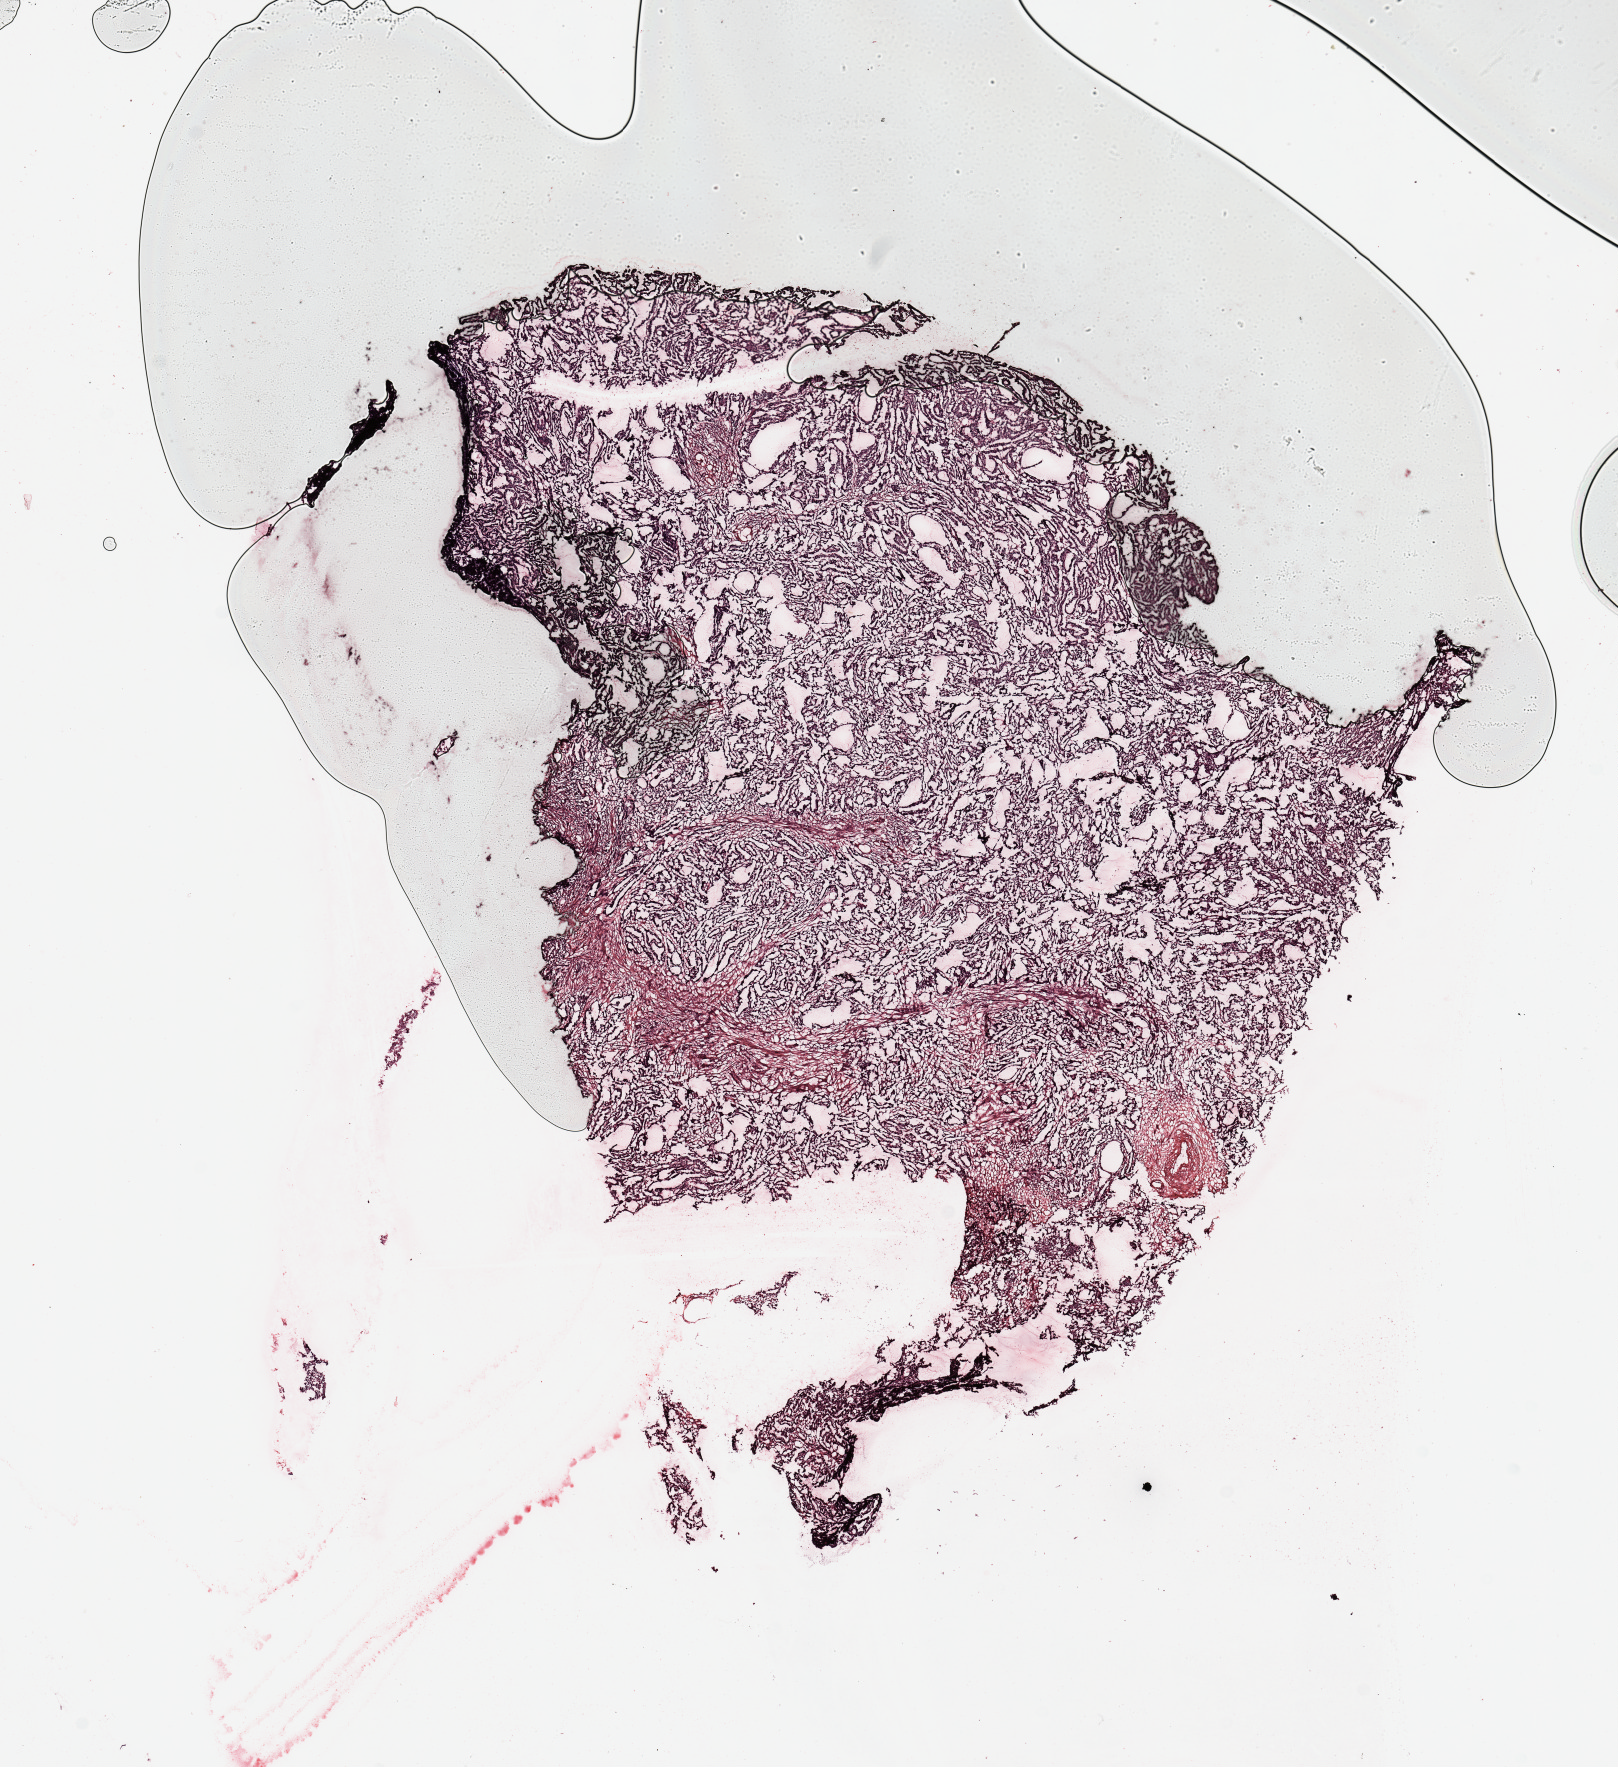
Whole-slide histology image, H&E-stained — whole scanned area (about 12.8 x 14.0 mm) shown as a low-resolution overview, tumour tissue sample, sampled site: uterus. 64-year-old female patient. Histologic grade: G1 (well differentiated). Pathologist review of this section (percent, as recorded): tumour nuclei 90%, necrosis 0%.
- AJCC pathologic stage: I
- histologic diagnosis: Endometrioid adenocarcinoma, NOS